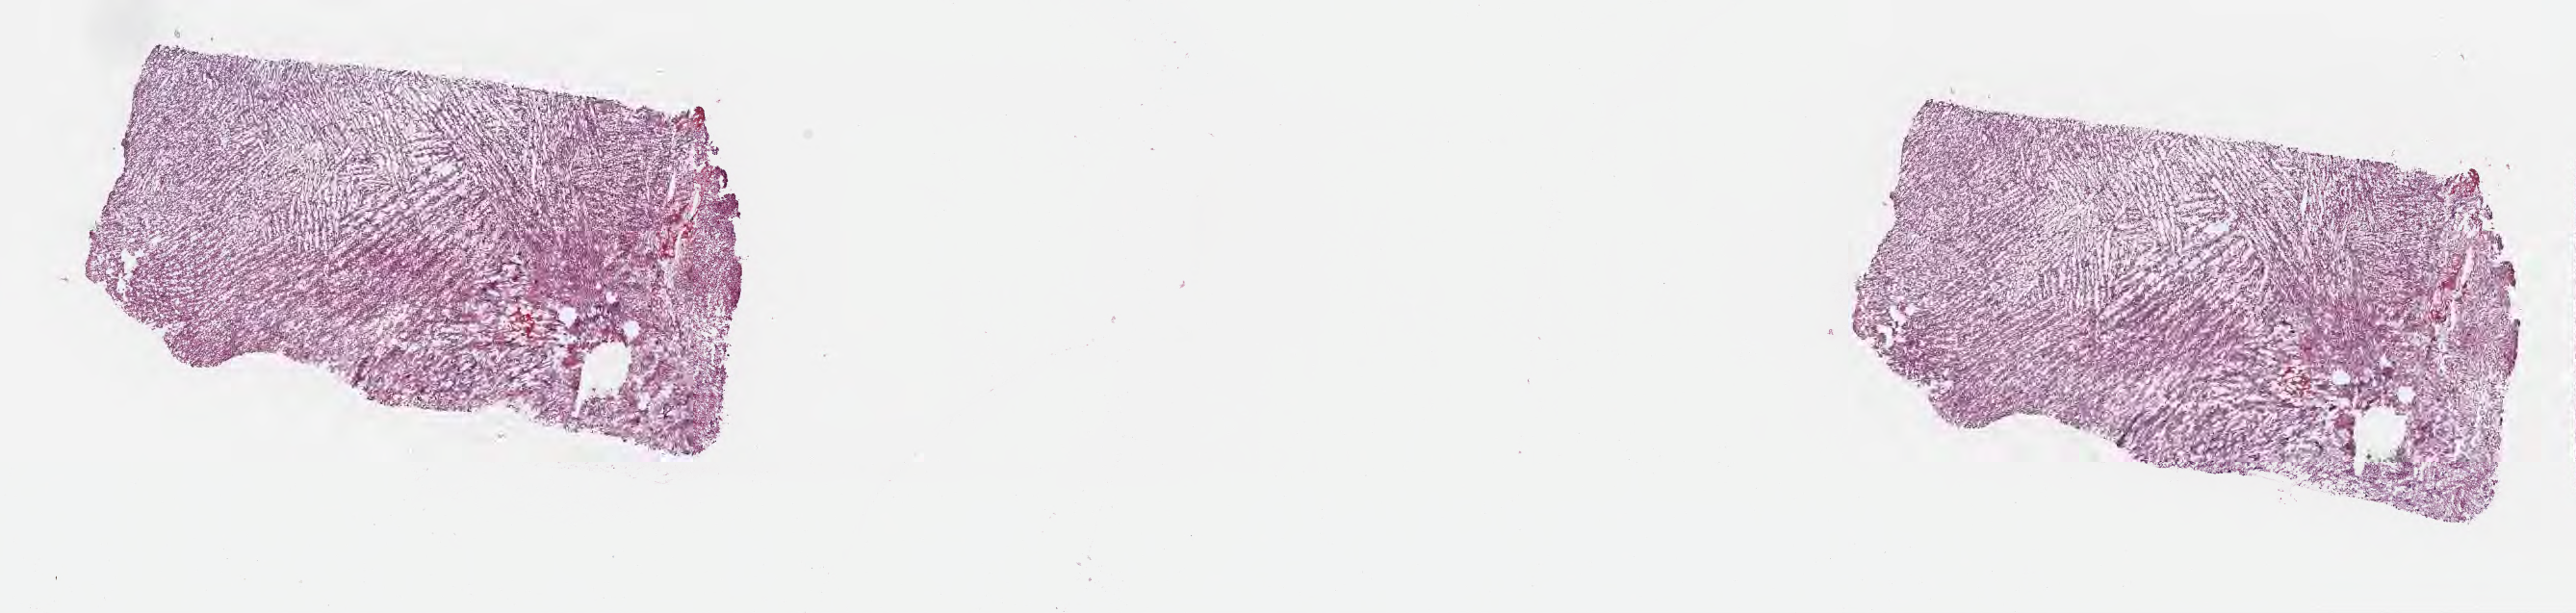
H&E whole-slide image — shown as a low-resolution overview of the whole scanned area (about 21.6 x 5.2 mm); cryosection; specimen: recurrent tumor; anatomic site: brain. Patient: female, age at initial diagnosis 58 years. Slide review estimates, as recorded: tumor cells 95%, tumor nuclei 96%, stromal cells 1%, necrosis 0%, normal cells 4%. Infiltration values recorded for this section: lymphocyte infiltration 0%, monocyte infiltration 0%, neutrophil infiltration 0%.
• section: top of the tissue portion
• patient diagnosis: Glioblastoma, NOS